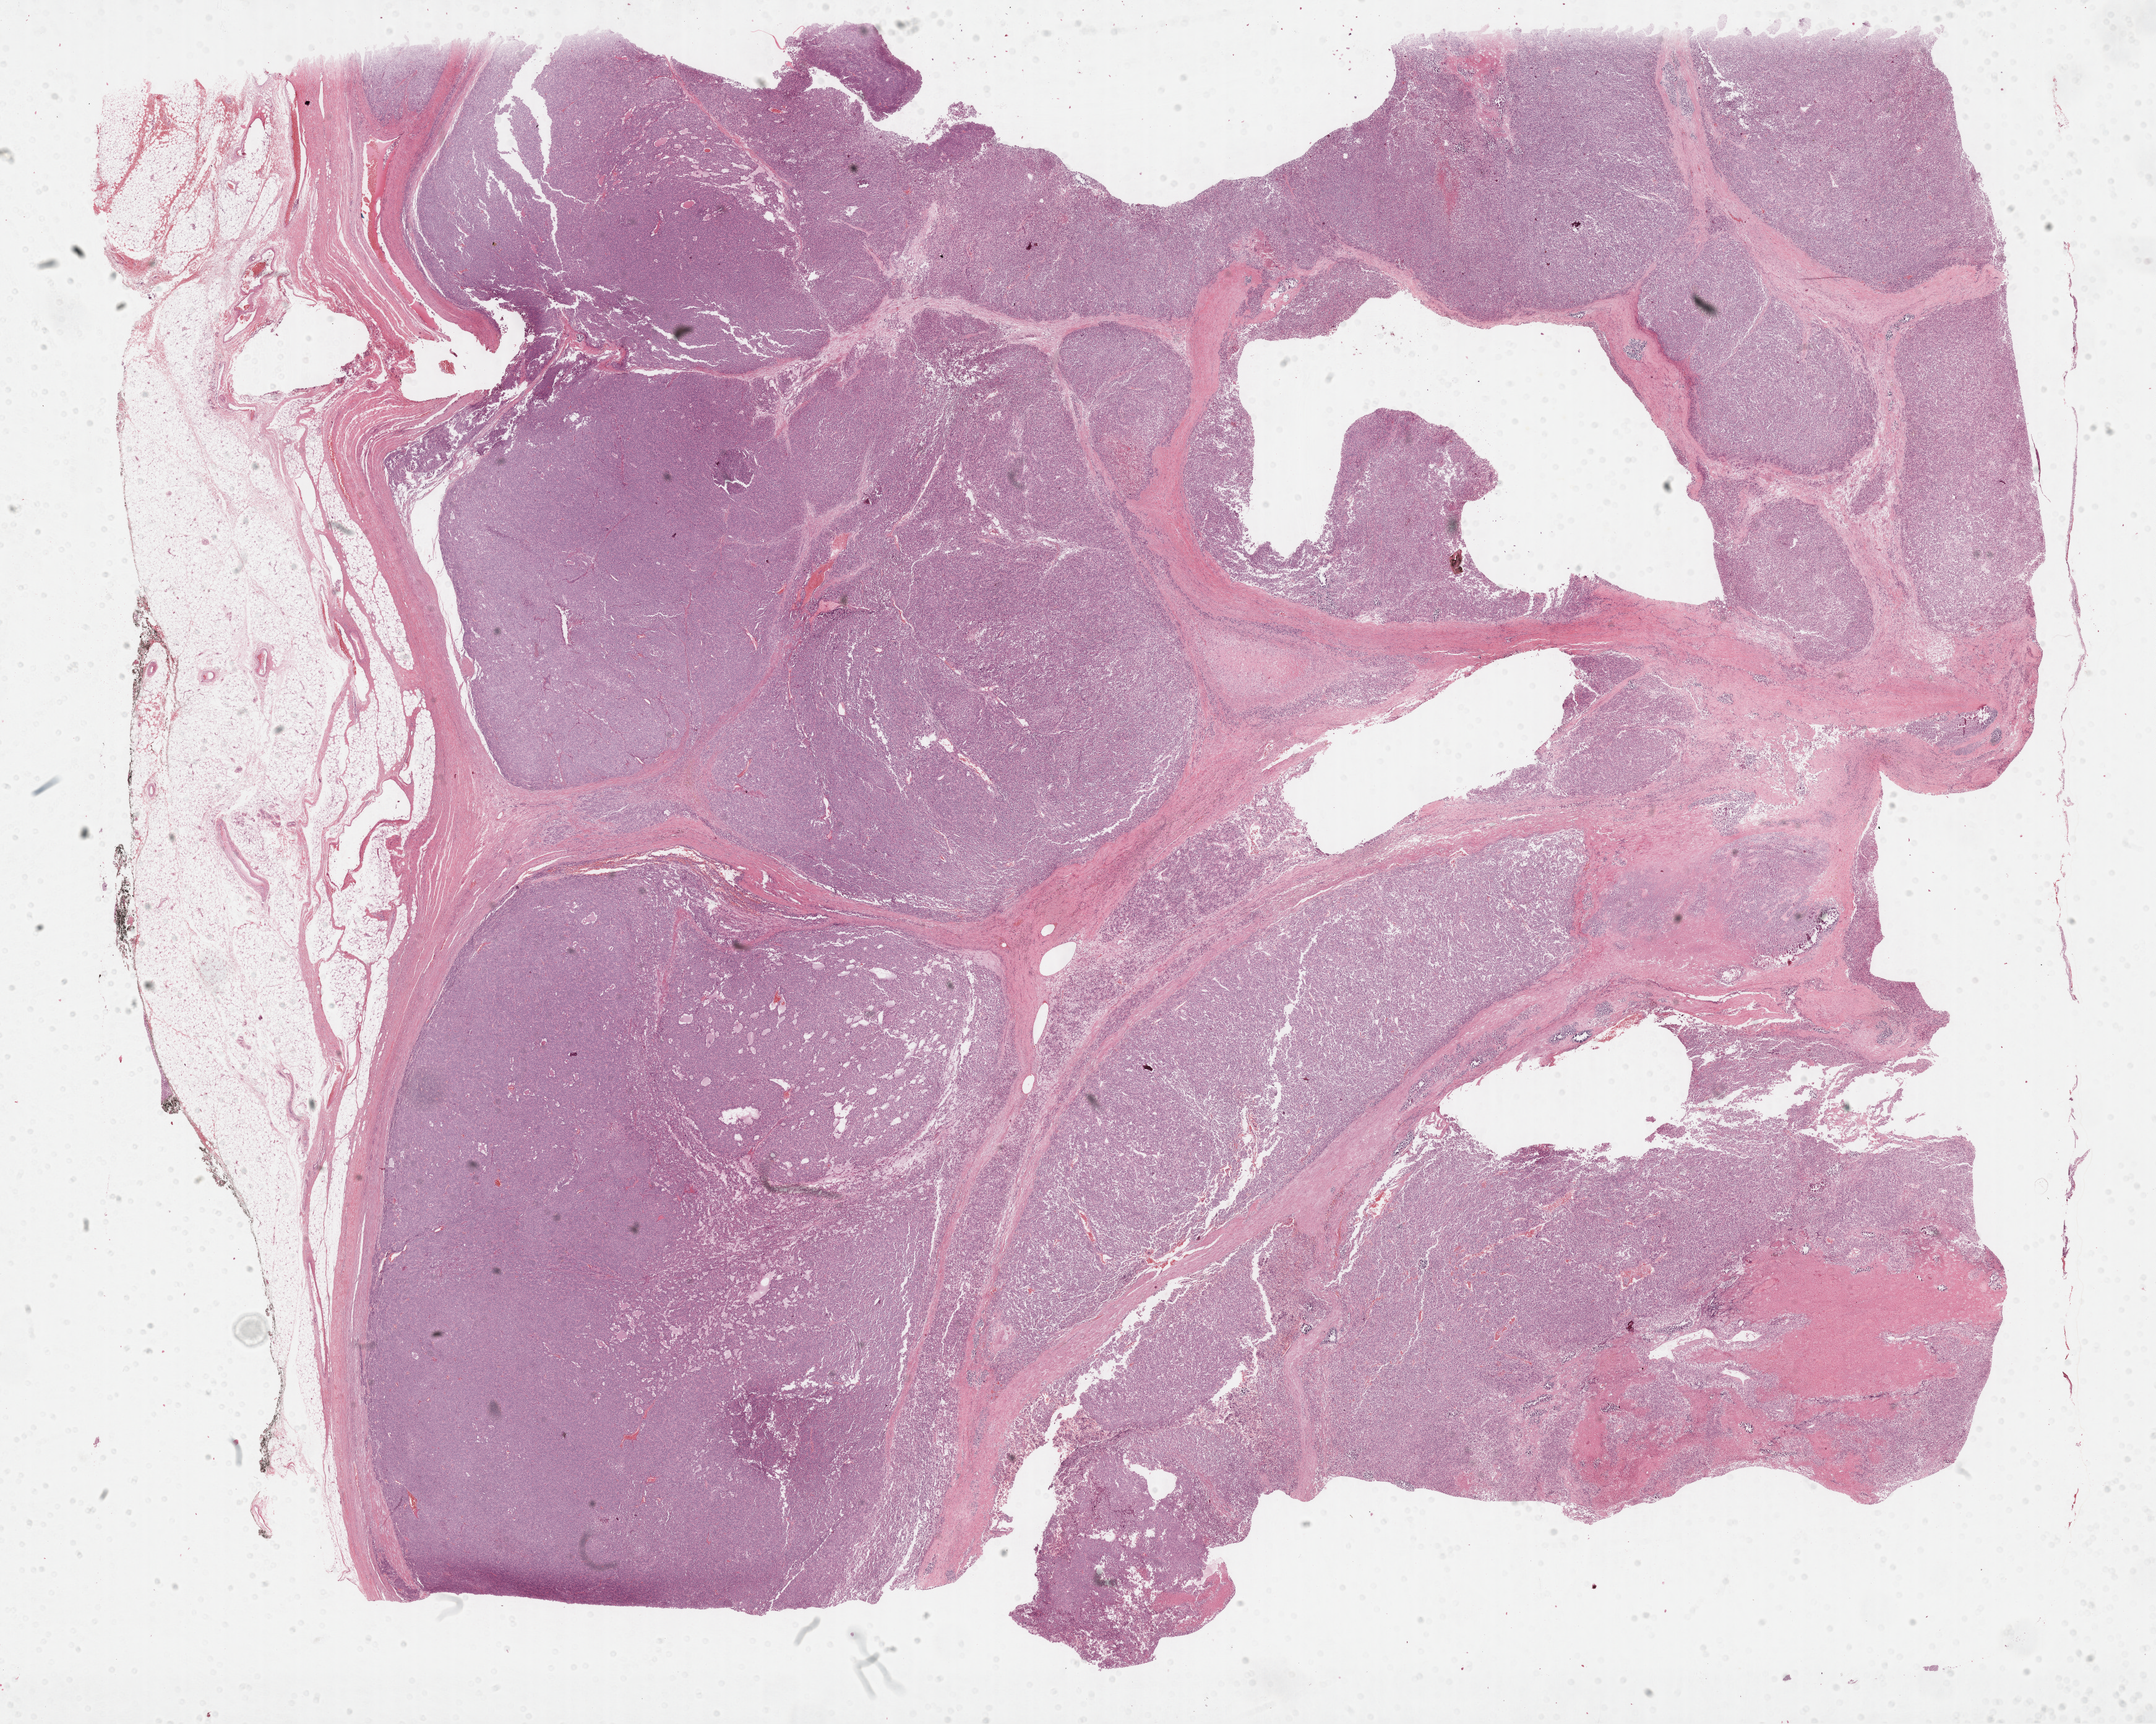
Hematoxylin and eosin (H&E) stained whole-slide image — whole scanned area (about 28.2 x 22.5 mm, acquisition: 40x scan) shown as a low-resolution overview. FFPE section. Sample: primary tumour, adrenal cortex. Female, age 22 years at initial diagnosis.
Histologic diagnosis: Adrenal cortical carcinoma (cortex of adrenal gland).